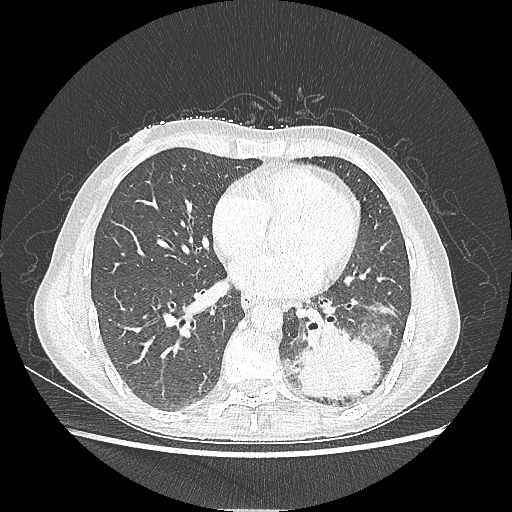
Chest CT, one axial slice. Slice 94 of 220 in the series (ordered by position). Lung window (W 1500 / L -600 HU). 1.25 mm slice thickness. 512 × 512 image matrix, field of view 360 × 360 mm. Patient: female, 53 years. From the clinical record (not read from this slice): clinical TNM (as recorded): T3 N0 M0.
Outlined on this slice (rectangle marked by the reading radiologist):
- lung tumour (recorded histology: adenocarcinoma): box from (x=291, y=320) to (x=384, y=401) px